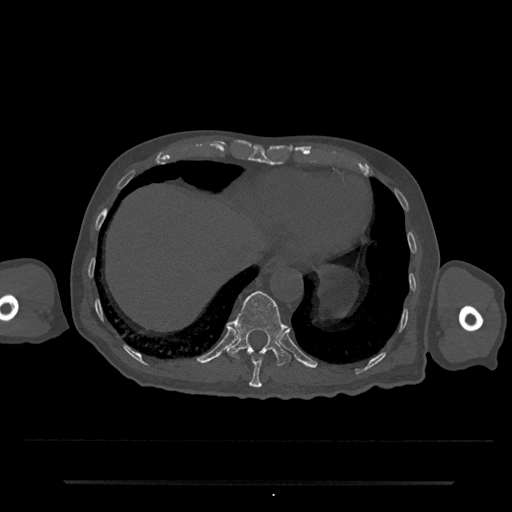
CT including the spine, one axial slice. Slice 273 of 797 in the series (ordered by position). 120 kVp. Bone window (W 1800 / L 400 HU). 512 × 512 image matrix, field of view 427 × 427 mm. Patient: male, 74 years. From the clinical record (not read from this slice): primary cancer: prostate.
Annotated regions visible in this slice (semi-automatic segmentation, software-assisted and operator-edited):
- T10 vertebra: bounding box <249,356,264,388> (left, top, right, bottom; pixels)
- T11 vertebra: <227,291,291,366>